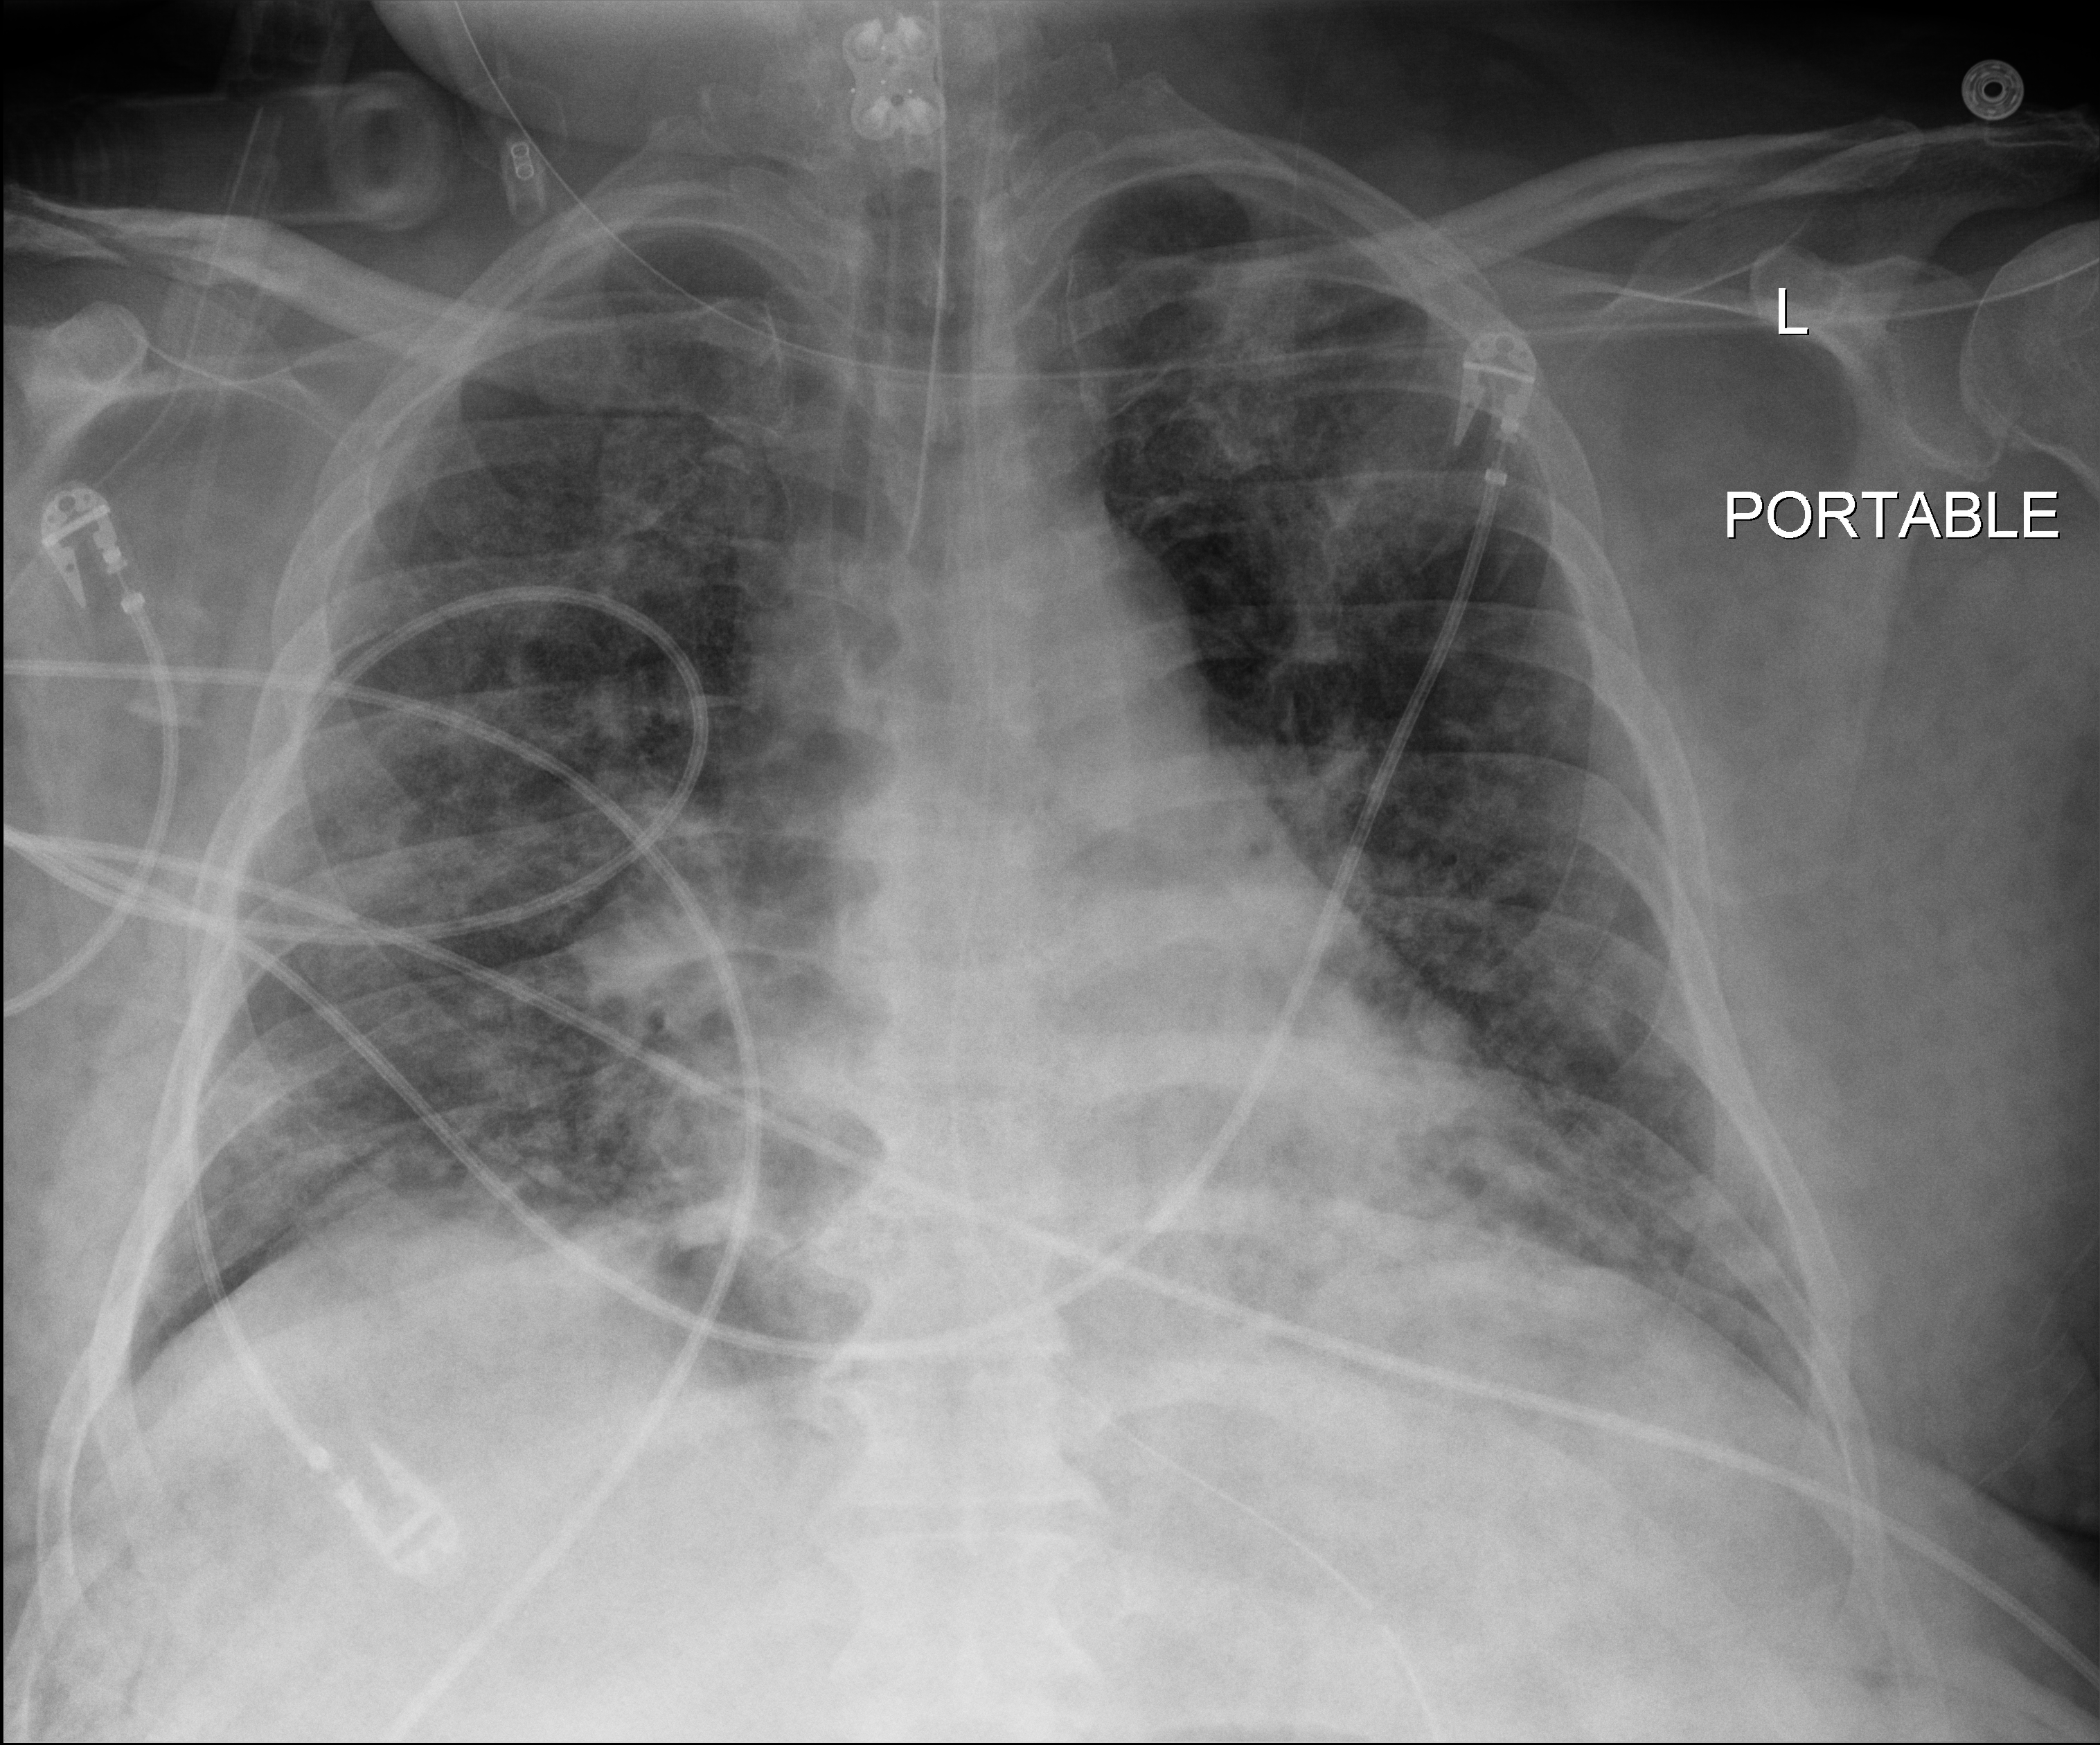
Portable chest radiograph. Male patient hospitalised with COVID-19, age 18–59 years.
From the hospital-stay record, not from the radiograph (when in the stay this image was taken is not recorded):
- mechanically ventilated during this hospital stay: yes